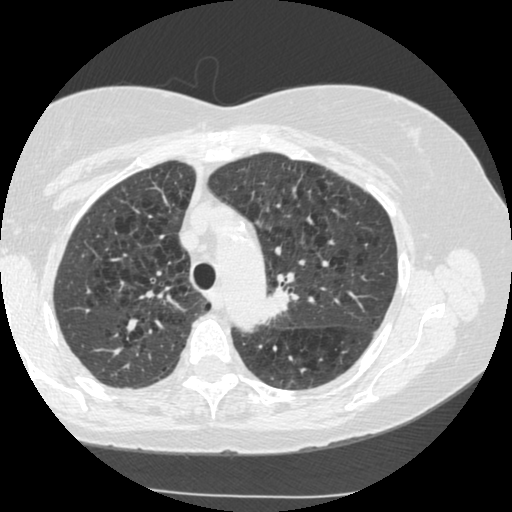
Low-dose screening chest CT, axial slice, second annual screen, lung window (W 1500 / L -600 HU), 1.25 mm slice thickness, standard (soft-tissue) reconstruction kernel (STANDARD), 120 kVp, slice 192 of 249 in the series, 512 × 512 image matrix. Female, age 70 years at enrolment. Current smoker at enrolment.
- Expert-annotated lung lesion, bounding box (x1, y1, x2, y2) in pixels: (241, 269, 305, 332).
- Reader record for this screening exam (exam-level; its link to the box is not recorded): non-calcified nodule or mass ≥4 mm, left upper lobe, 15 × 13 mm, spiculated (stellate) margins, soft tissue attenuation, pre-existing on the prior screen: yes; interval growth: yes.
- Official screen result: positive, other.
- Later outcome: lung cancer diagnosed 360 days after this screen — neoplasm, malignant, left upper lobe, stage IIIB (AJCC 6th edition), 40 mm at pathology.